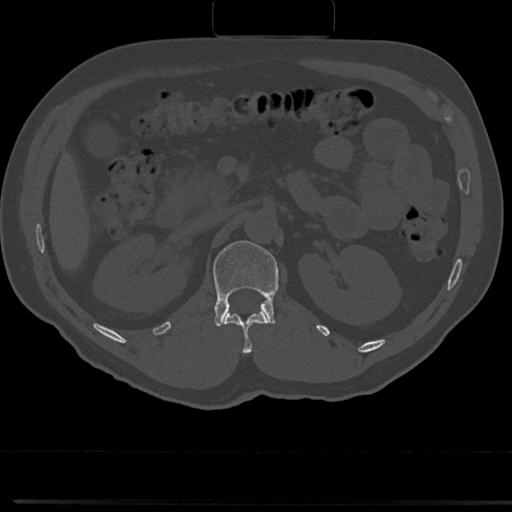
CT including the spine, one axial slice; reconstruction kernel Br40s/3; 120 kVp; bone window (W 1800 / L 400 HU); 512 × 512 image matrix, field of view 355 × 355 mm. Male patient, age 61 years. Case-level facts recorded for this patient, not image findings: primary cancer: prostate.
Structures marked on this image (semi-automatically segmented with operator editing):
- L1 vertebra: bounding box <191,240,278,327> (left, top, right, bottom; pixels)
- T12 vertebra: <225,312,268,352>